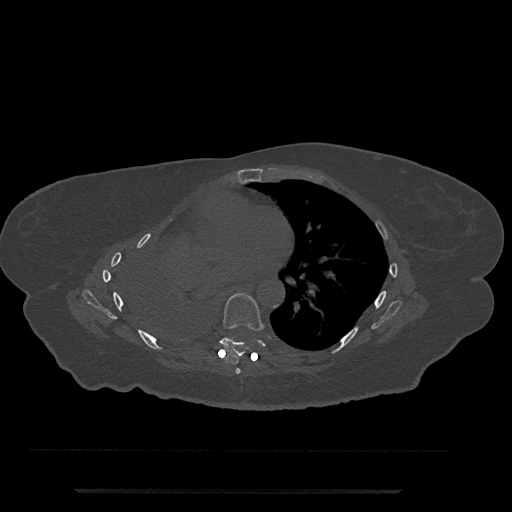
CT including the spine, one axial slice; slice 438 of 797 in the series (ordered by position); 120 kVp; bone window (W 1800 / L 400 HU); 0.5 mm slice thickness; 512 × 512 image matrix, field of view 440 × 440 mm. Female patient, age 51 years. Case-level facts recorded for this patient, not image findings: primary cancer: neuro; vertebrae with lytic lesions (as recorded): T8.
Outlined on this slice (semi-automatic segmentation, software-assisted and operator-edited):
- T6 vertebra: bounding box <235,368,241,374> (left, top, right, bottom; pixels)
- T7 vertebra: <219,293,266,357>